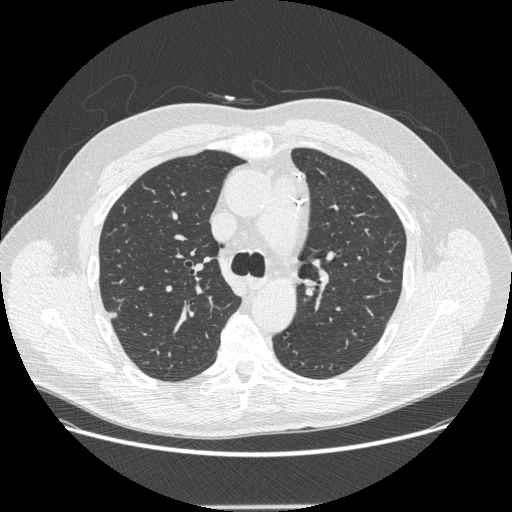
Low-dose screening chest CT, one axial slice. Position 191 of 265 along the scan axis. 120 kVp. Lung window (W 1500 / L -600 HU). 512 × 512 image matrix, field of view 400 × 400 mm.
Structures marked on this image (outlined manually by an expert reader):
- lesion 1 (tumor, upper lobe of right lung): box from (x=109, y=311) to (x=118, y=319) px